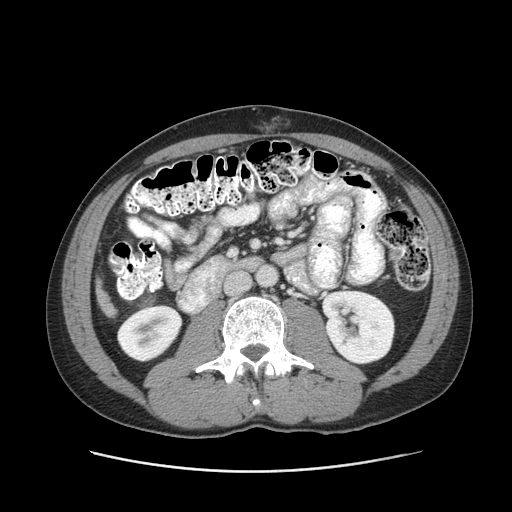
Contrast-enhanced abdominal CT (liver protocol), one axial slice. Slice 23 of 93 in the series (ordered by position). Reconstruction kernel STANDARD. 120 kVp. Soft-tissue window (W 400 / L 40 HU). 512 × 512 image matrix, field of view 380 × 380 mm. From the clinical record (not read from this slice): diagnosis: hepatocellular carcinoma (patient treated with transarterial chemoembolisation; whether this scan precedes or follows treatment is not stated here); TNM stage (as recorded): Stage-II; Child-Pugh class: A; tumour differentiation: moderately differentiated; tumour nodularity: multinodular.
Structures marked on this image (semi-automatic segmentation, software-assisted and operator-edited):
- liver parenchyma outside the tumour (the mass and vessels are separate outlines, so this box may not span the whole liver): bounding box <96,278,114,316> (left, top, right, bottom; pixels)